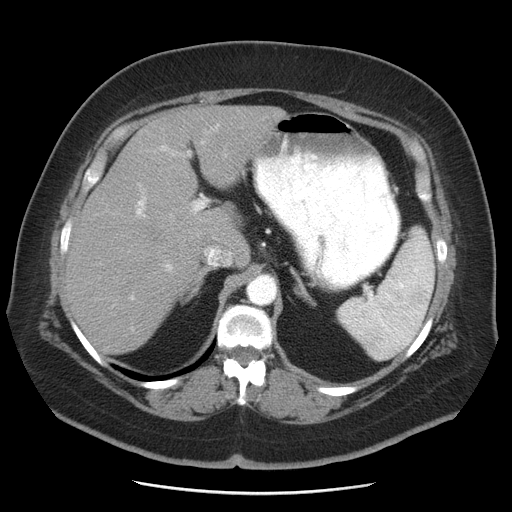
Contrast-enhanced abdominal CT, one axial slice. Slice 32 of 55 in the series (ordered by position). 120 kVp. Soft-tissue window (W 400 / L 40 HU). 512 × 512 image matrix. Female patient, age 52 years. Case-level facts recorded for this patient, not image findings: diagnosis: colorectal cancer liver metastases, imaged before liver resection; multiple liver metastases: yes; largest metastasis: 2.5 cm; chemotherapy before resection: no.
Outlined on this slice (manually delineated by an expert):
- liver: bounding box [x1, y1, x2, y2] px = [66, 106, 288, 355]
- planned liver remnant (the part of the liver to remain after resection): [66, 182, 206, 355]
- portal vein (with intrahepatic branches): [131, 140, 212, 299]